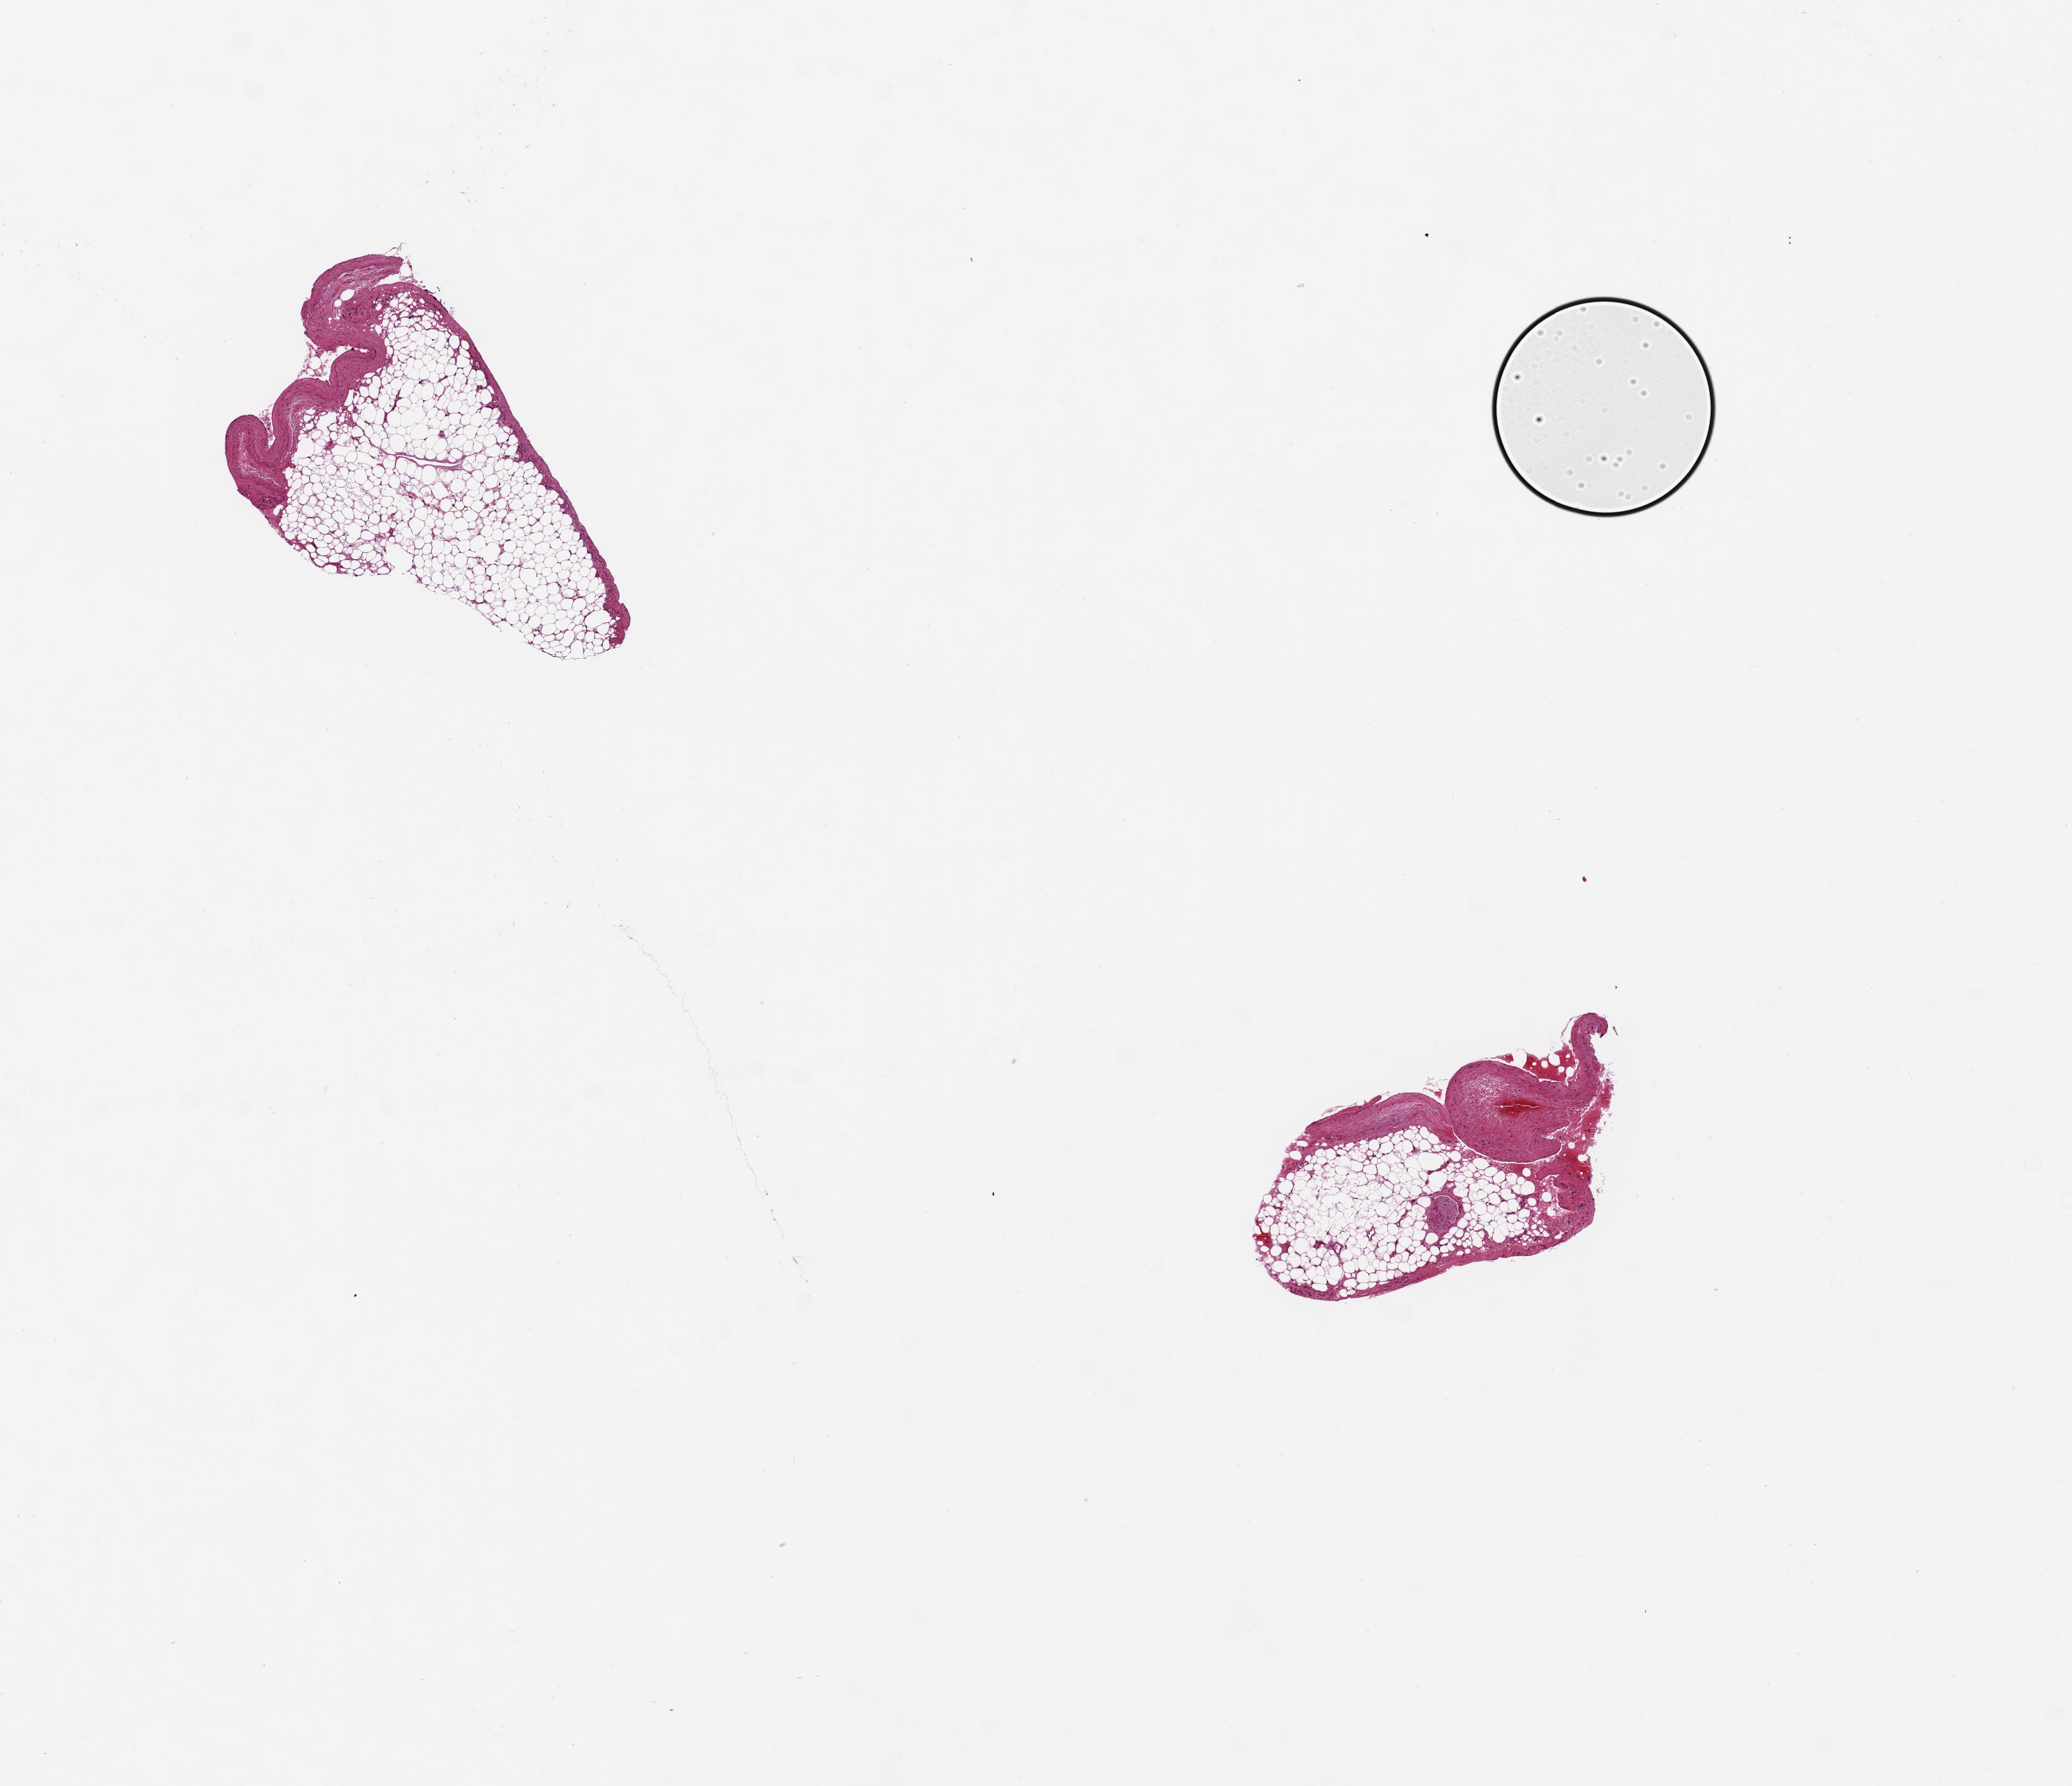
Whole-slide image, hematoxylin and eosin (H&E) stain, shown as a low-resolution overview of the whole scanned area (about 11.8 x 10.2 mm). PAXgene-fixed paraffin-embedded (PFPE) section. Sampled site (target tissue): coronary artery. Donor tissue sample. Donor: male.
Reviewer comment on this tissue sample: 2 pieces, 3x2 & 2x1mm; >90% adipose.